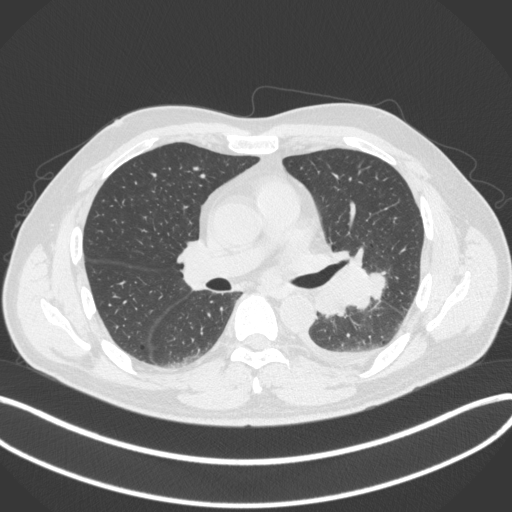
Chest CT, one axial slice. Slice 202 of 350 in the series (ordered by position). Reconstruction kernel B31f. Lung window (W 1500 / L -600 HU). 1 mm slice thickness. 512 × 512 image matrix, field of view 400 × 400 mm. Patient: male, 58 years. Case-level facts recorded for this patient, not image findings: clinical TNM (as recorded): T3 N1 M1b.
Outlined on this slice (bounding box drawn by a radiologist):
- lung tumour (recorded histology: small cell carcinoma): bounding box <315,249,387,317> (left, top, right, bottom; pixels)